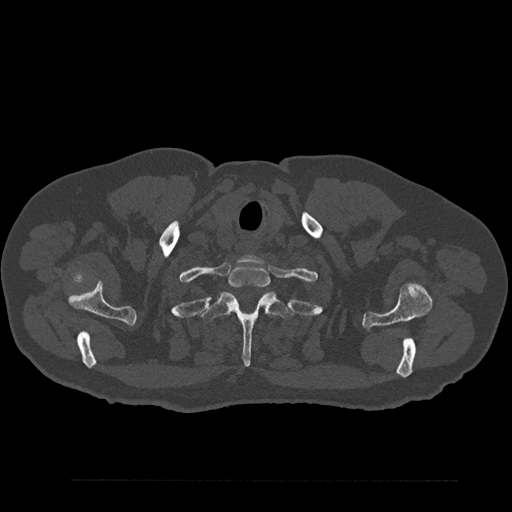
CT including the spine, one axial slice; slice 734 of 797 in the series (ordered by position); reconstruction kernel Br40s/3; bone window (W 1800 / L 400 HU); 0.5 mm slice thickness; 512 × 512 image matrix, field of view 430 × 430 mm. Male patient, age 61 years. Case-level facts recorded for this patient, not image findings: primary cancer: prostate.
Outlined on this slice (semi-automatically segmented with operator editing):
- T1 vertebra: box from (x=228, y=264) to (x=270, y=288) px
- T2 vertebra: (x=201, y=292)–(x=294, y=366)